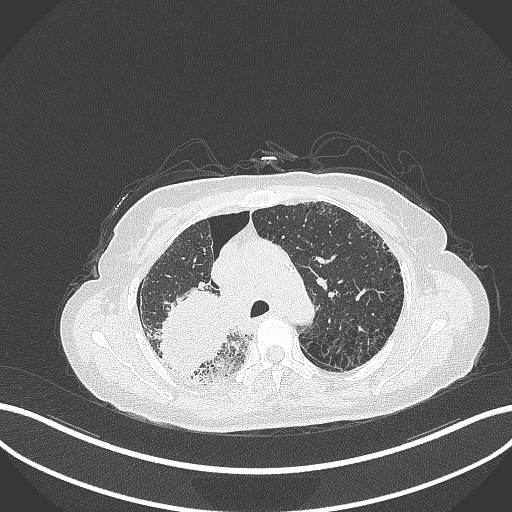
Chest CT, one axial slice. Slice 249 of 408 in the series (ordered by position). Reconstruction kernel B70f. 120 kVp. Lung window (W 1500 / L -600 HU). 1 mm slice thickness. 512 × 512 image matrix. Female patient, age 64 years. From the clinical record (not read from this slice): clinical TNM (as recorded): T3 N3 M0.
Structures marked on this image (bounding box drawn by a radiologist):
- lung tumour (recorded histology: squamous cell carcinoma): bounding box <155,284,231,380> (left, top, right, bottom; pixels)